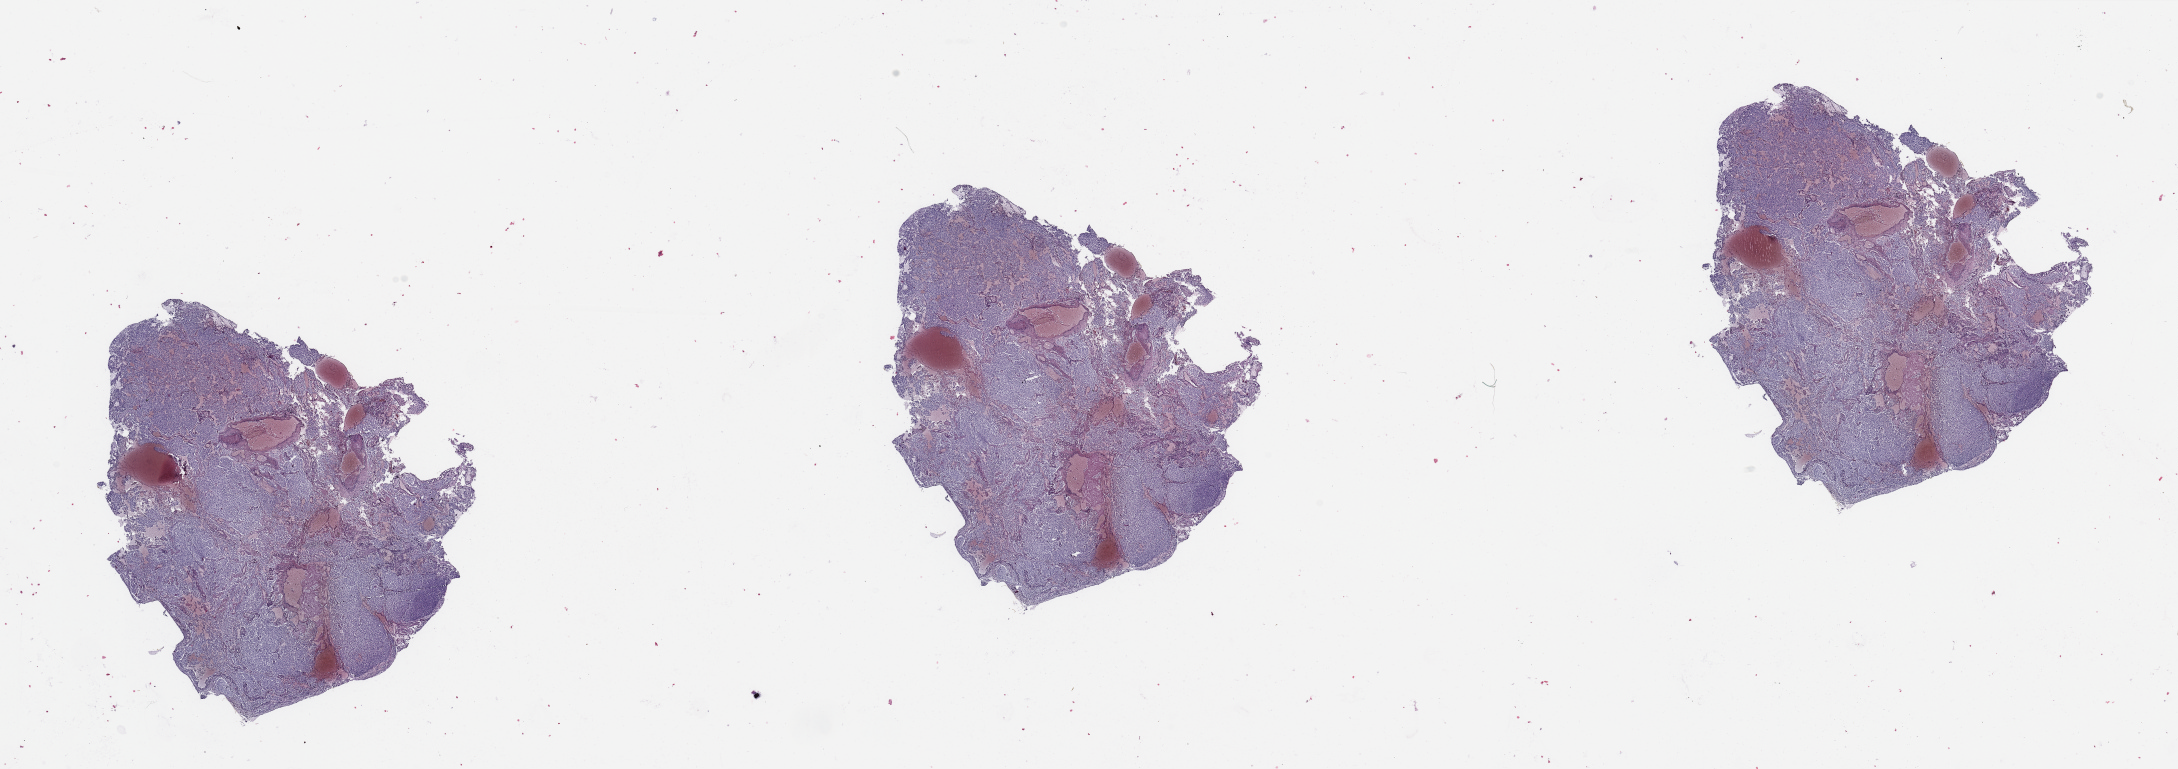
H&E-stained whole-slide image, shown as a low-resolution overview of the whole scanned area (about 34.5 x 12.2 mm, acquisition: 20x scan), tumour tissue sample, sampled site: brain. Male, 40 y/o. Composition of this section per pathologist review: tumour nuclei 80%, necrosis 20%.
Histologic diagnosis: Glioblastoma.